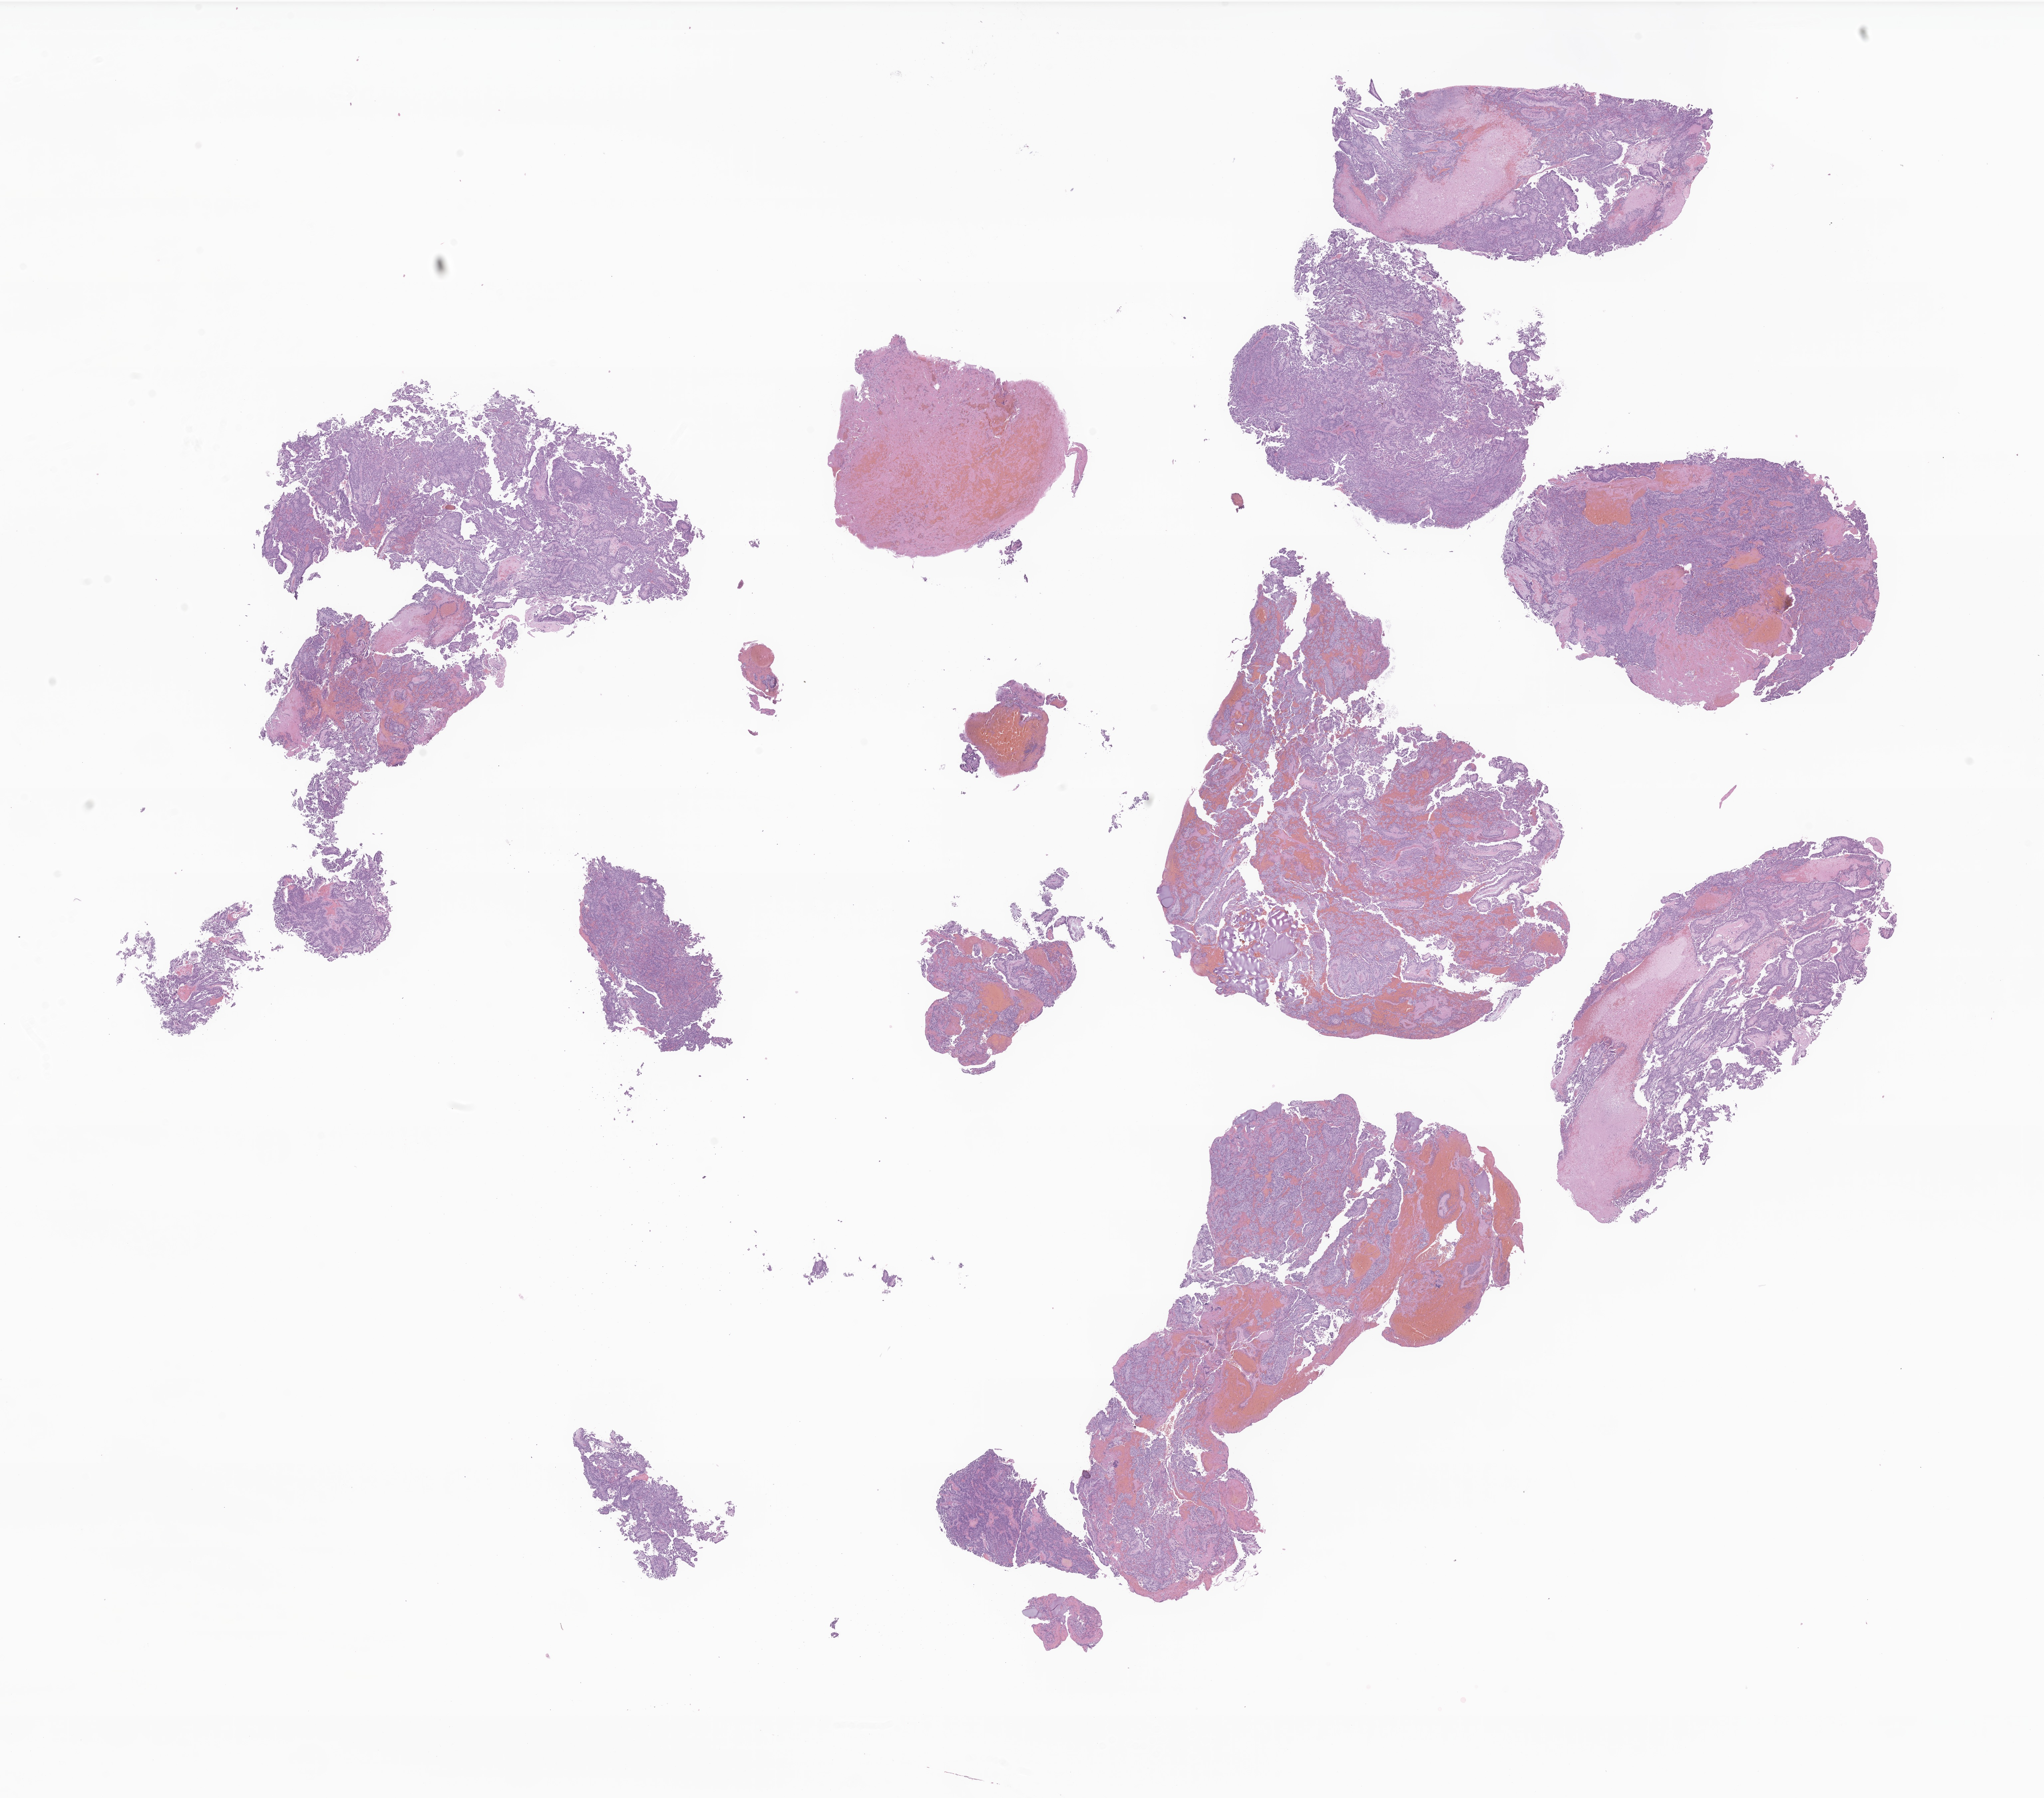
Haematoxylin and eosin whole-slide image of tumor tissue from the brain, a low-resolution overview of the entire scanned area, about 25.9 x 22.8 mm. FFPE section. Patient: male, age 142 months (11 years 10 months).
Diagnosis: Ependymoma, NOS.